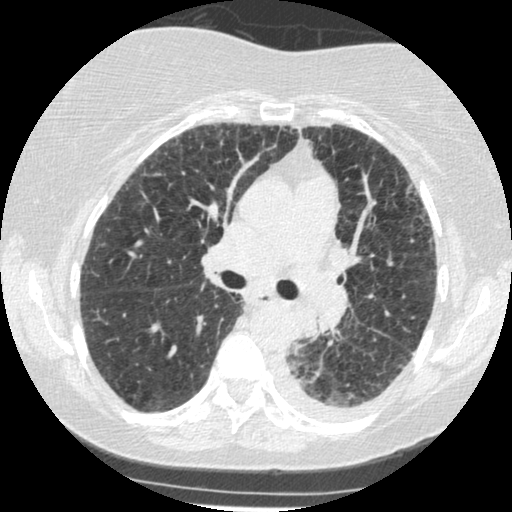
Low-dose screening chest CT, axial slice, third annual screen, lung window (W 1500 / L -600 HU), 120 kVp, 512 × 512 image matrix, field of view 310 × 310 mm. Female participant, aged 60 years at enrolment. Former smoker at enrolment.
Lesion marked by an expert reader, bounding box (x1, y1, x2, y2) in pixels: (268, 308, 342, 373). Screening reader's record for this exam (one nodule recorded; not confirmed to be the boxed lesion): non-calcified nodule or mass ≥4 mm, left lower lobe, 54 × 38 mm, smooth margins, soft tissue attenuation, pre-existing on the prior screen: yes; interval growth: yes. Official screen result: positive, other. Participant outcome: lung cancer diagnosed 15 days after this screen — small cell carcinoma, NOS, left lower lobe, undifferentiated (G4), stage IV (AJCC 6th edition), 69 mm at pathology.